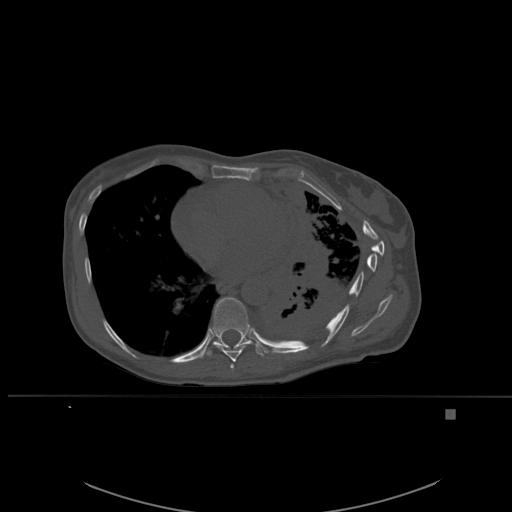
CT including the spine, one axial slice; slice 342 of 537 in the series (ordered by position); bone window (W 1800 / L 400 HU); 1.5 mm slice thickness; 512 × 512 image matrix, field of view 440 × 440 mm. Patient: female, 45 years. From the clinical record (not read from this slice): primary cancer: lung.
Outlined on this slice (semi-automatic segmentation, software-assisted and operator-edited):
- T7 vertebra: bounding box <230,364,234,370> (left, top, right, bottom; pixels)
- T8 vertebra: <212,344,249,362>
- T9 vertebra: <202,297,266,359>